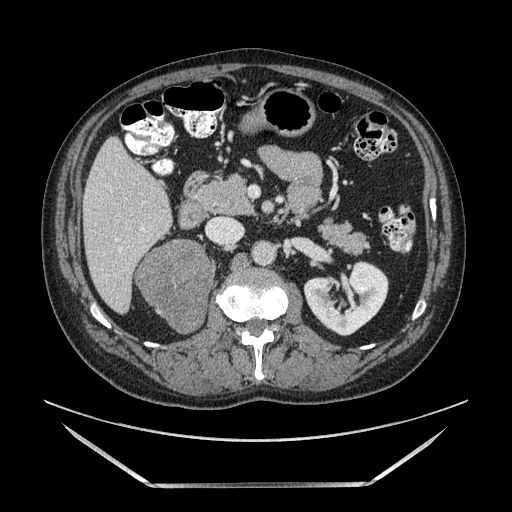
Contrast-enhanced abdominal CT, one axial slice. Slice 60 of 185 in the series (ordered by position). Soft-tissue window (W 400 / L 40 HU). 1.25 mm slice thickness. 512 × 512 image matrix. Male patient. From the clinical record (not read from this slice): diagnosis: adrenocortical carcinoma; tumour side: right adrenal; tumour size at pathology: 10.3 cm; Ki-67 index: 20 %; stage (as recorded): 3.
Outlined on this slice (semi-automatically segmented with operator editing):
- mass: bounding box <137,241,213,334> (left, top, right, bottom; pixels)